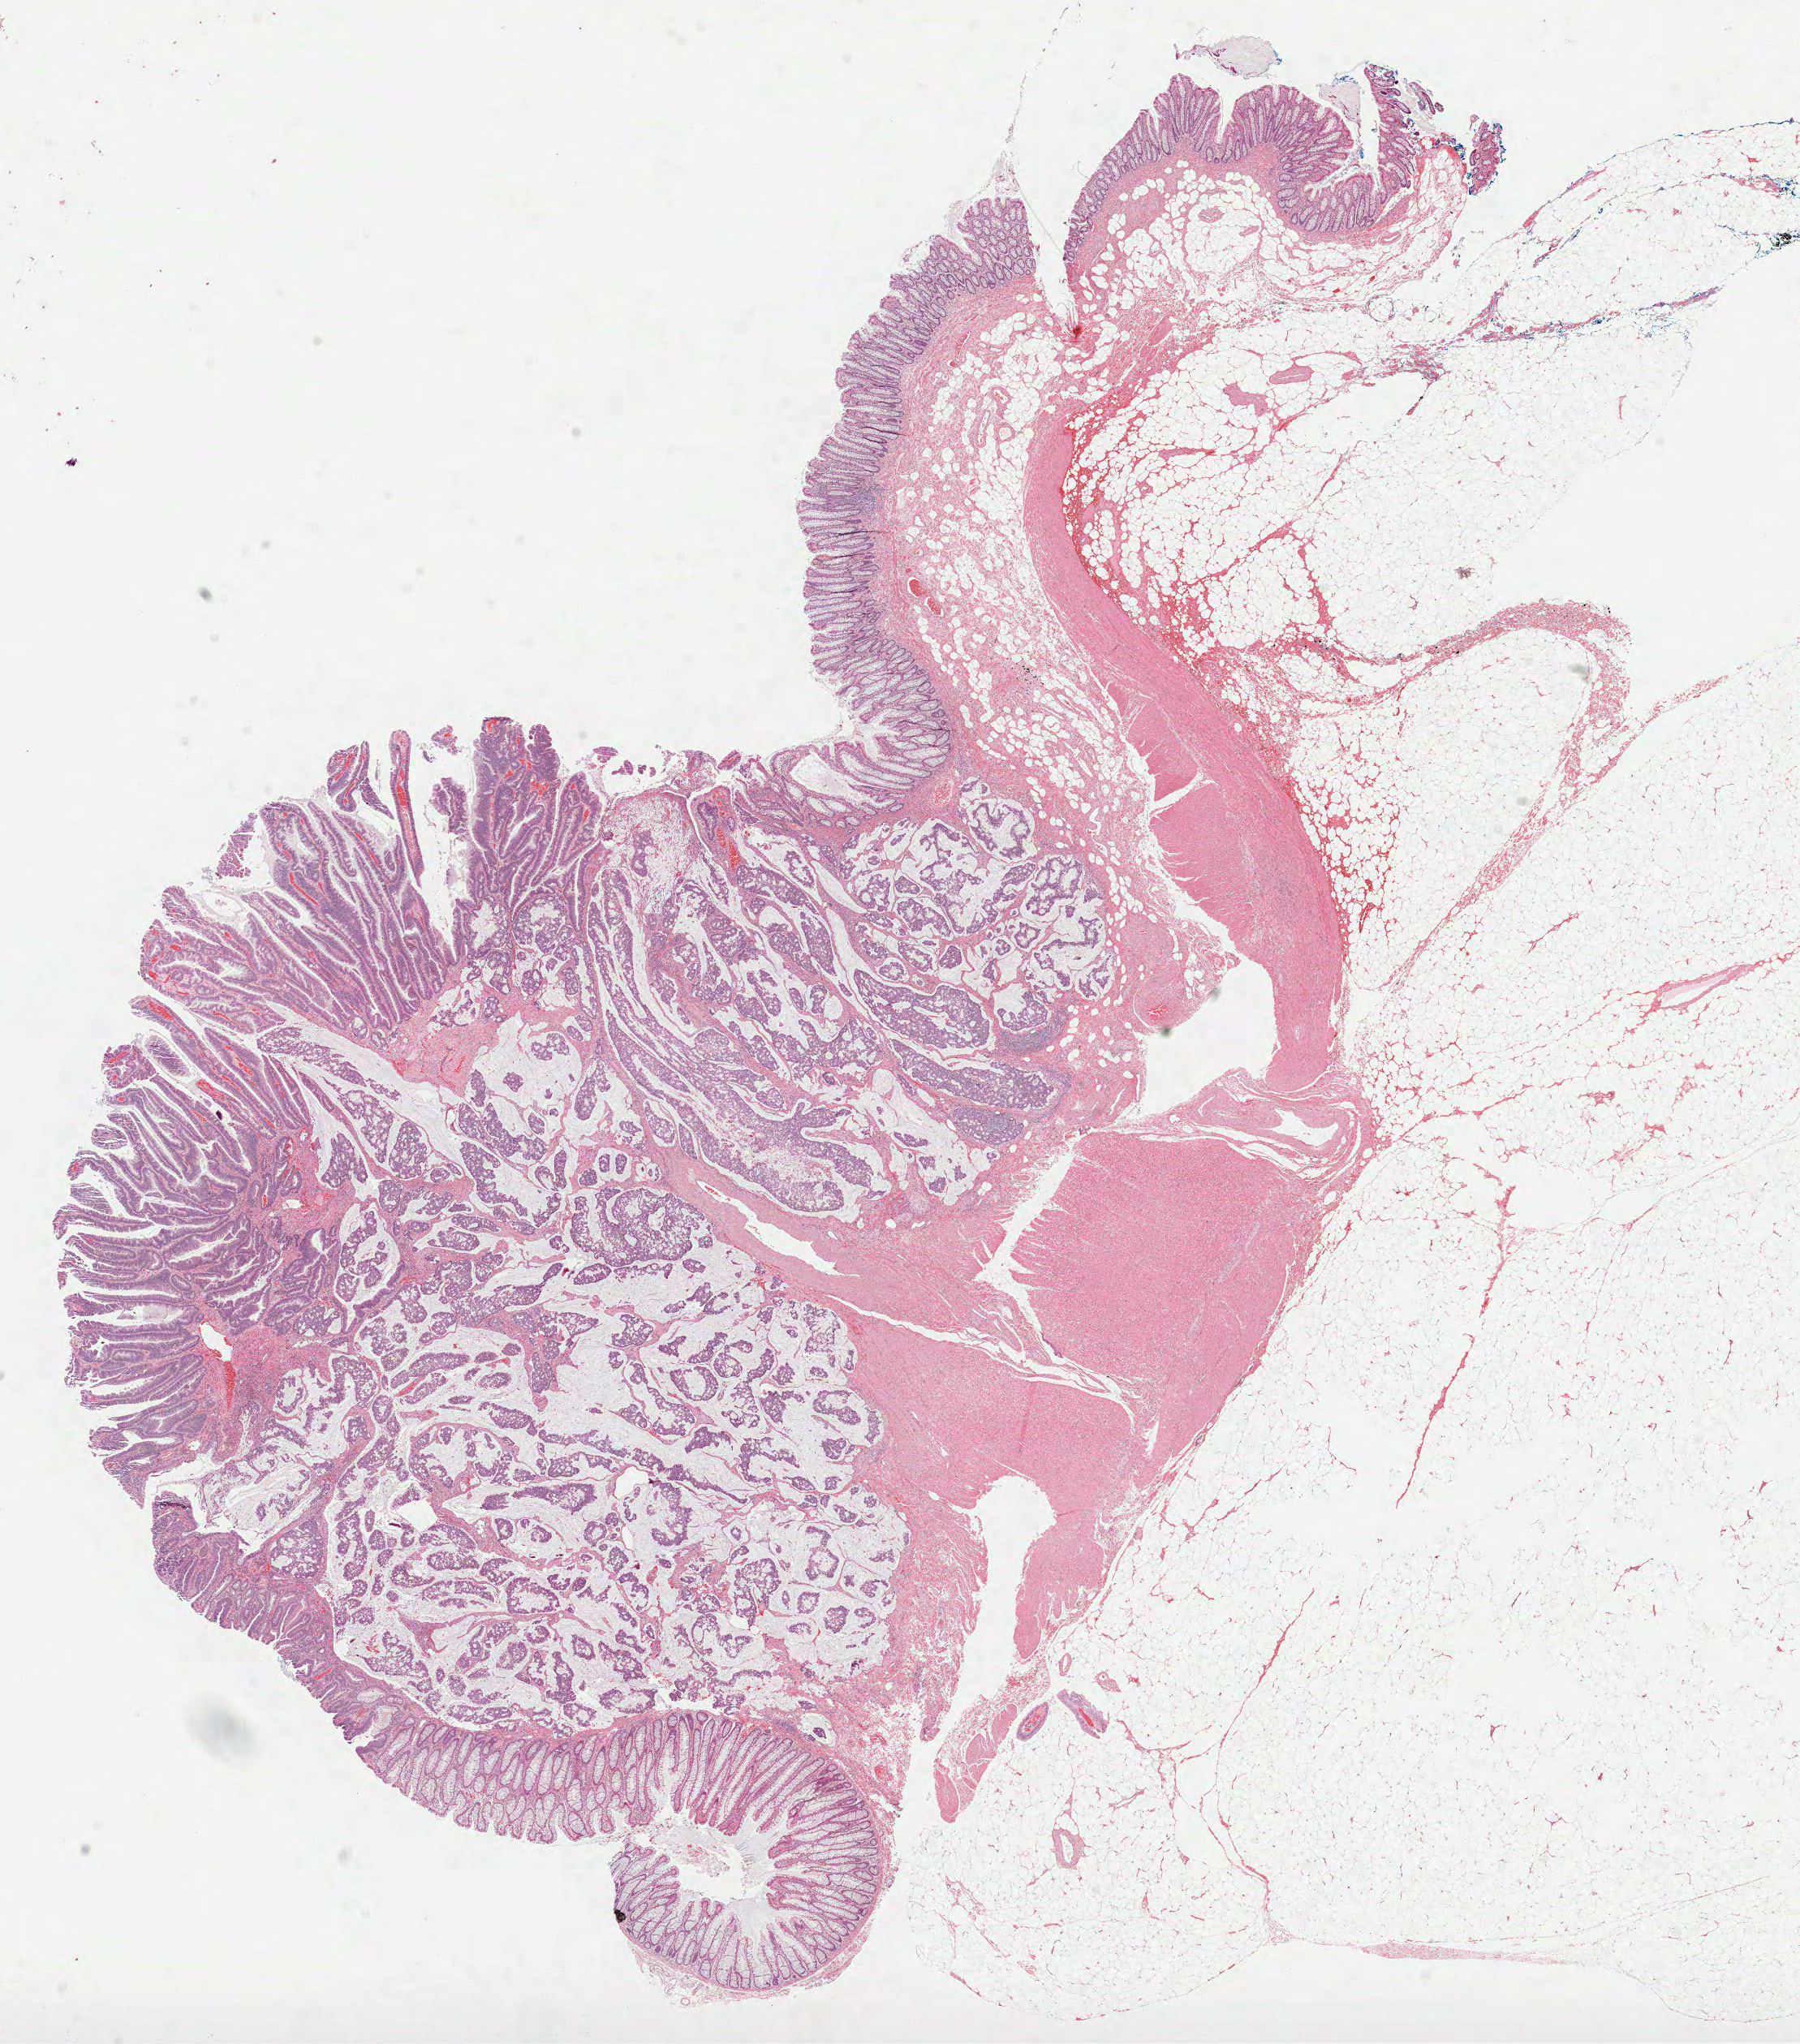
Whole-slide histology image, H&E — shown as a low-resolution overview of the whole scanned area (about 17.9 x 20.3 mm). Formalin-fixed paraffin-embedded (FFPE) diagnostic section. Rectum, primary tumour sample. Patient: male, age at initial diagnosis 67 years.
• lymph nodes positive (case pathology): 1 of 26 examined
• pathologic diagnosis: Mucinous adenocarcinoma (rectosigmoid junction)
• TNM: T1 N1 MX
• AJCC pathologic stage: IIIA (6th edition)